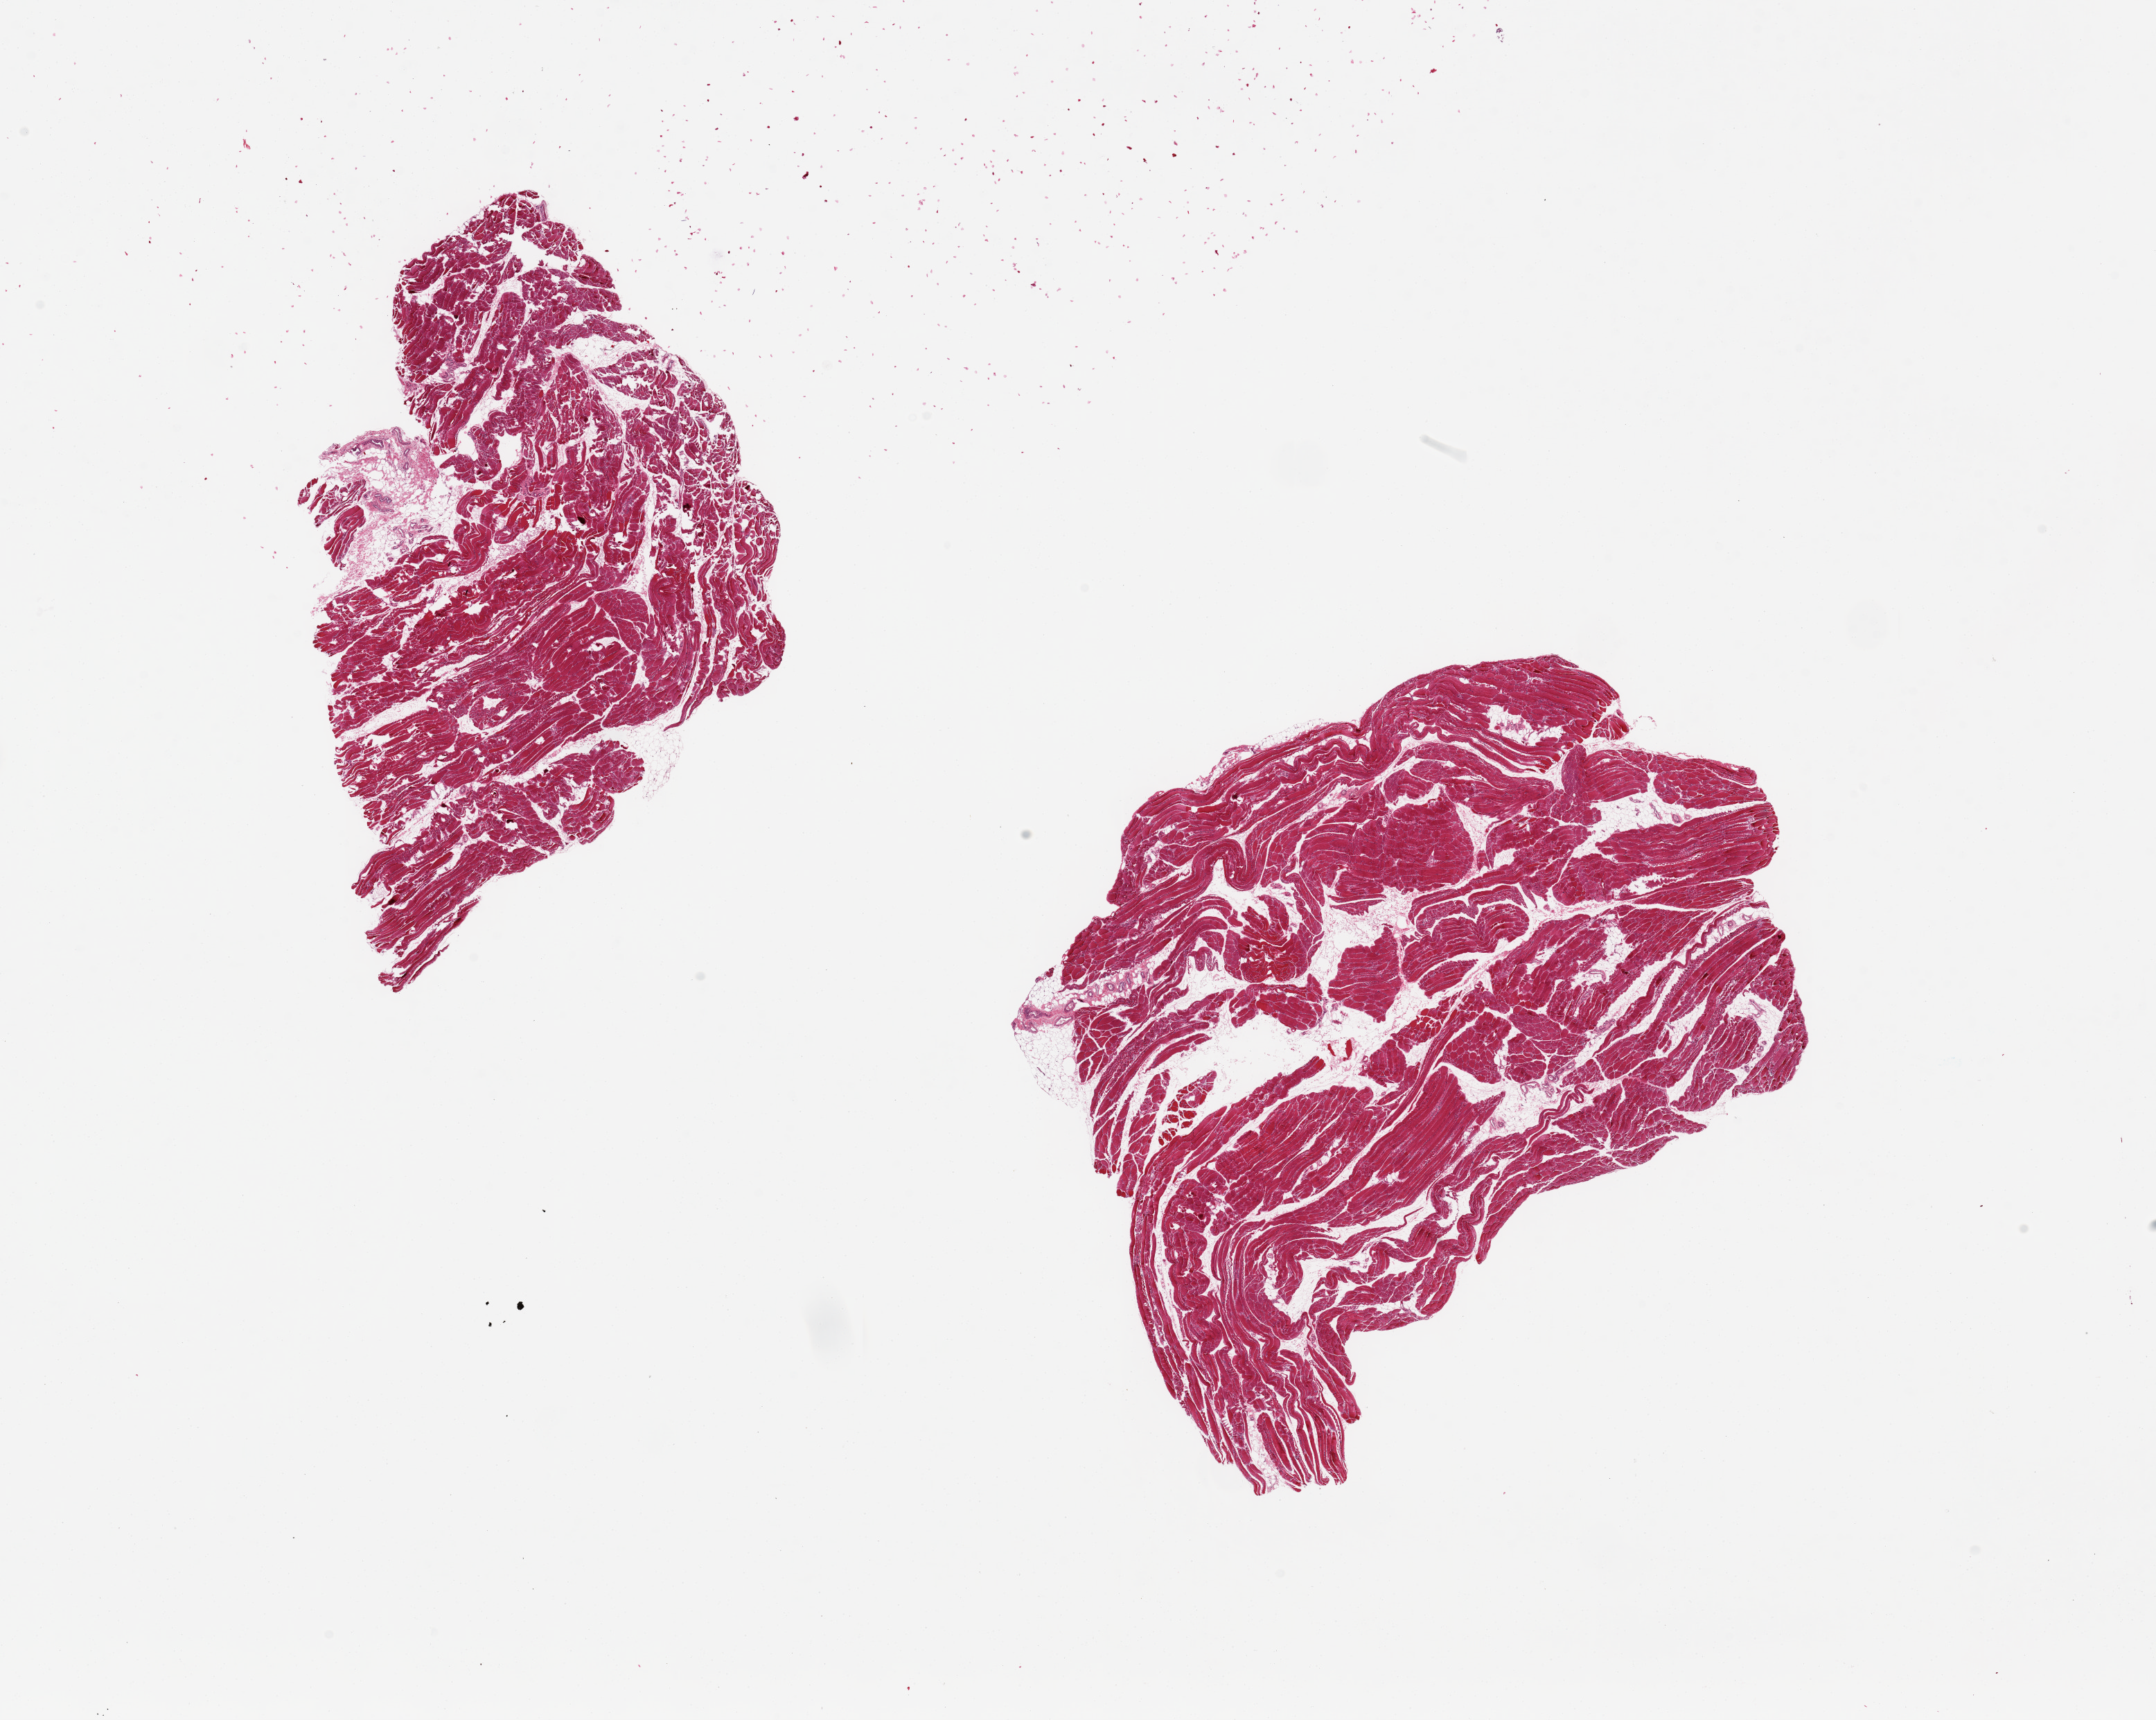
Digitized hematoxylin and eosin (H&E)-stained section, low-resolution overview of the scanned area, about 24.6 x 19.6 mm (slide scanned at 20x); PAXgene-fixed, paraffin-embedded tissue; section of skeletal muscle (target tissue); donor tissue sample. Donor sex: female.
Review note (as recorded): 2 pieces, 9x6 & 10x9mm; ~35-40% interstitial fat.